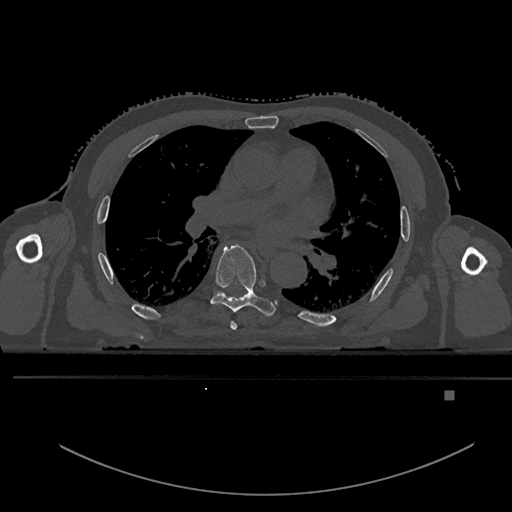
CT including the spine, one axial slice. Slice 309 of 969 in the series (ordered by position). Bone window (W 1800 / L 400 HU). 0.5 mm slice thickness. 512 × 512 image matrix, field of view 456 × 456 mm. Male patient, age 82 years. Case-level facts recorded for this patient, not image findings: primary cancer: prostate.
Annotated regions visible in this slice (semi-automatic segmentation, software-assisted and operator-edited):
- T5 vertebra: bounding box [x1, y1, x2, y2] px = [230, 321, 237, 330]
- T6 vertebra: [201, 245, 276, 317]